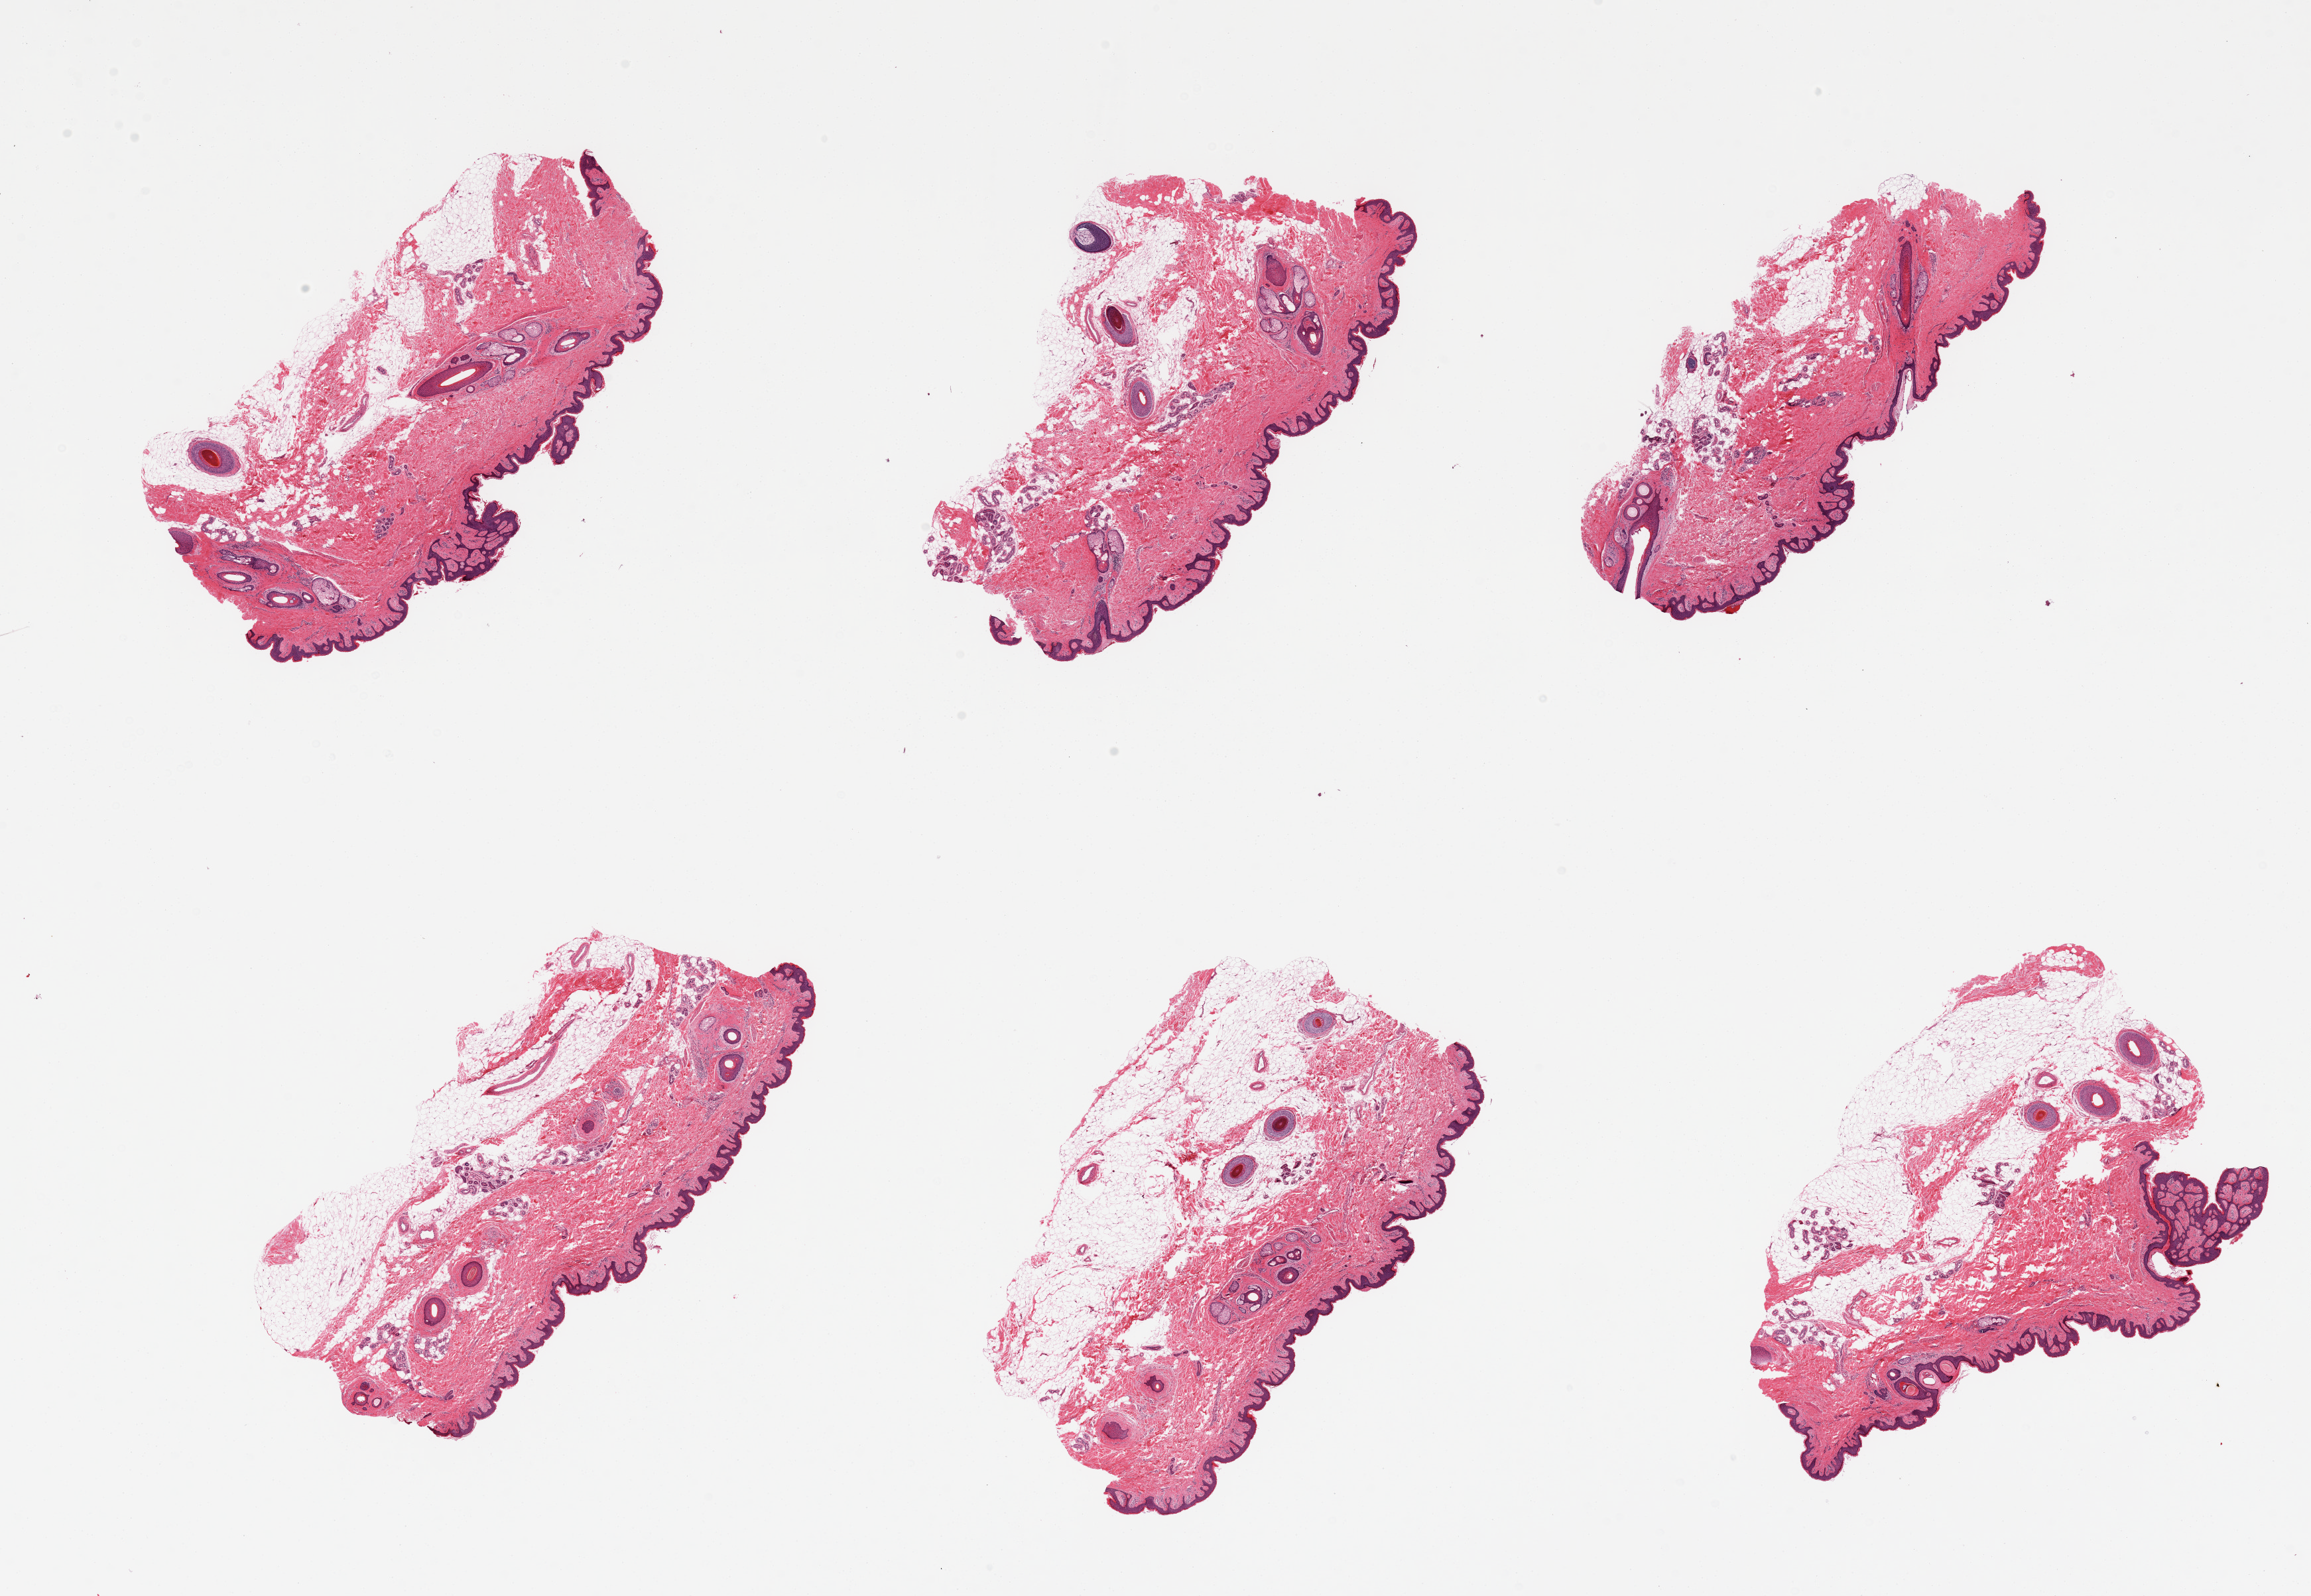
Digitized haematoxylin and eosin-stained section — whole scanned area (about 27.6 x 19.0 mm, acquisition: 20x scan) shown as a low-resolution overview, PAXgene-fixed paraffin-embedded (PFPE) section, section of skin of suprapubic region (target tissue), donor tissue sample. Male donor.
Pathologist's review note for this sample: 6 pieces, includes up to 50% predominantly attached adipose tissue, dermatophytes identified, fibroepithelial polyp.